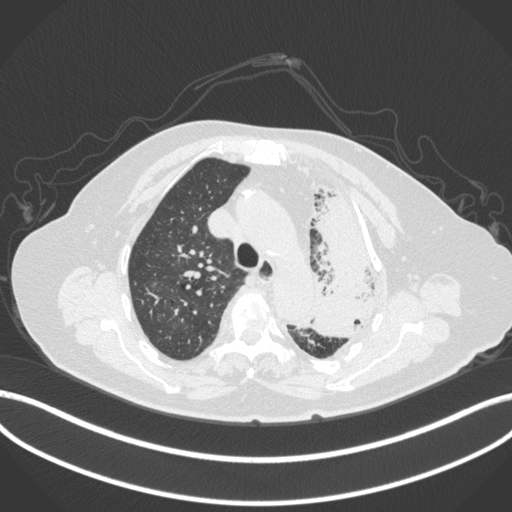
Chest CT, one axial slice; slice 291 of 399 in the series (ordered by position); reconstruction kernel B31f; 120 kVp; lung window (W 1500 / L -600 HU); 512 × 512 image matrix, field of view 400 × 400 mm. Female patient, age 75 years. Case-level facts recorded for this patient, not image findings: clinical TNM (as recorded): T3 N3 M1.
Outlined on this slice (rectangle marked by the reading radiologist):
- lung tumour (recorded histology: adenocarcinoma): bounding box [x1, y1, x2, y2] px = [306, 181, 386, 342]